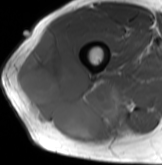
MRI of an extremity soft-tissue mass, one axial slice. Position 51 of 61 along the scan axis. MR volume resampled by the dataset authors to the PET/CT grid (not the native acquisition matrix). 3.27 mm slice thickness. 162 × 165 image matrix, field of view 158 × 161 mm. Male patient. Case-level facts recorded for this patient, not image findings: histological type: poorly differentiated synovial sarcoma; grade: high; site of the primary tumour: right buttock.
Structures marked on this image (expert contour drawn on MRI and transferred to this co-registered scan by the dataset authors):
- gross tumour volume including surrounding oedema: bounding box (x1, y1, x2, y2) in pixels: (14, 29, 122, 142)
- gross tumour volume (mass): (14, 29, 122, 142)